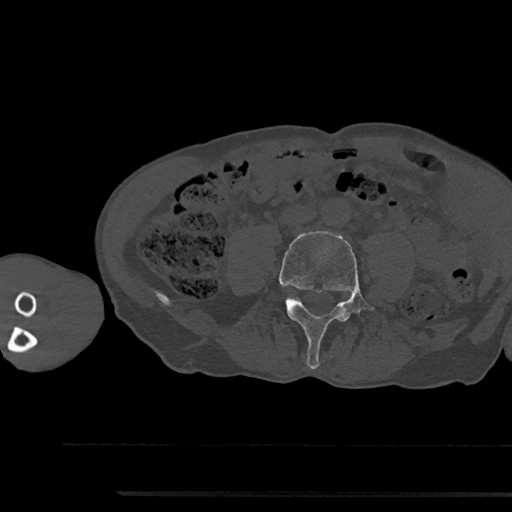
CT including the spine, one axial slice. Position 409 of 797 along the scan axis. Reconstruction kernel Br40s/3. 120 kVp. Bone window (W 1800 / L 400 HU). 512 × 512 image matrix, field of view 367 × 367 mm. Patient: male, 79 years. From the clinical record (not read from this slice): primary cancer: prostate.
Annotated regions visible in this slice (semi-automatically segmented with operator editing):
- L4 vertebra: bounding box [x1, y1, x2, y2] px = [278, 231, 375, 369]